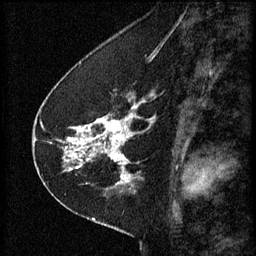
Breast MRI (dynamic contrast-enhanced), one sagittal slice; position 25 of 60 along the scan axis; 3 images stored at this slice position (order not interpretable as contrast timing); 1.5 T; TE 4.2 ms, TR 8.2 ms; 2 mm slice thickness; 256 × 256 image matrix, field of view 180 × 180 mm. Female patient, age 41 years.
Annotated regions visible in this slice (semi-automatic segmentation, software-assisted and operator-edited):
- analysis volume of interest (the breast-tissue region the enhancement analysis was run in; not a lesion): box from (x=67, y=98) to (x=152, y=173) px
- tumour enhancement mask (voxels above the 70 % enhancement threshold inside the analysis volume of interest): (x=67, y=106)–(x=152, y=171)